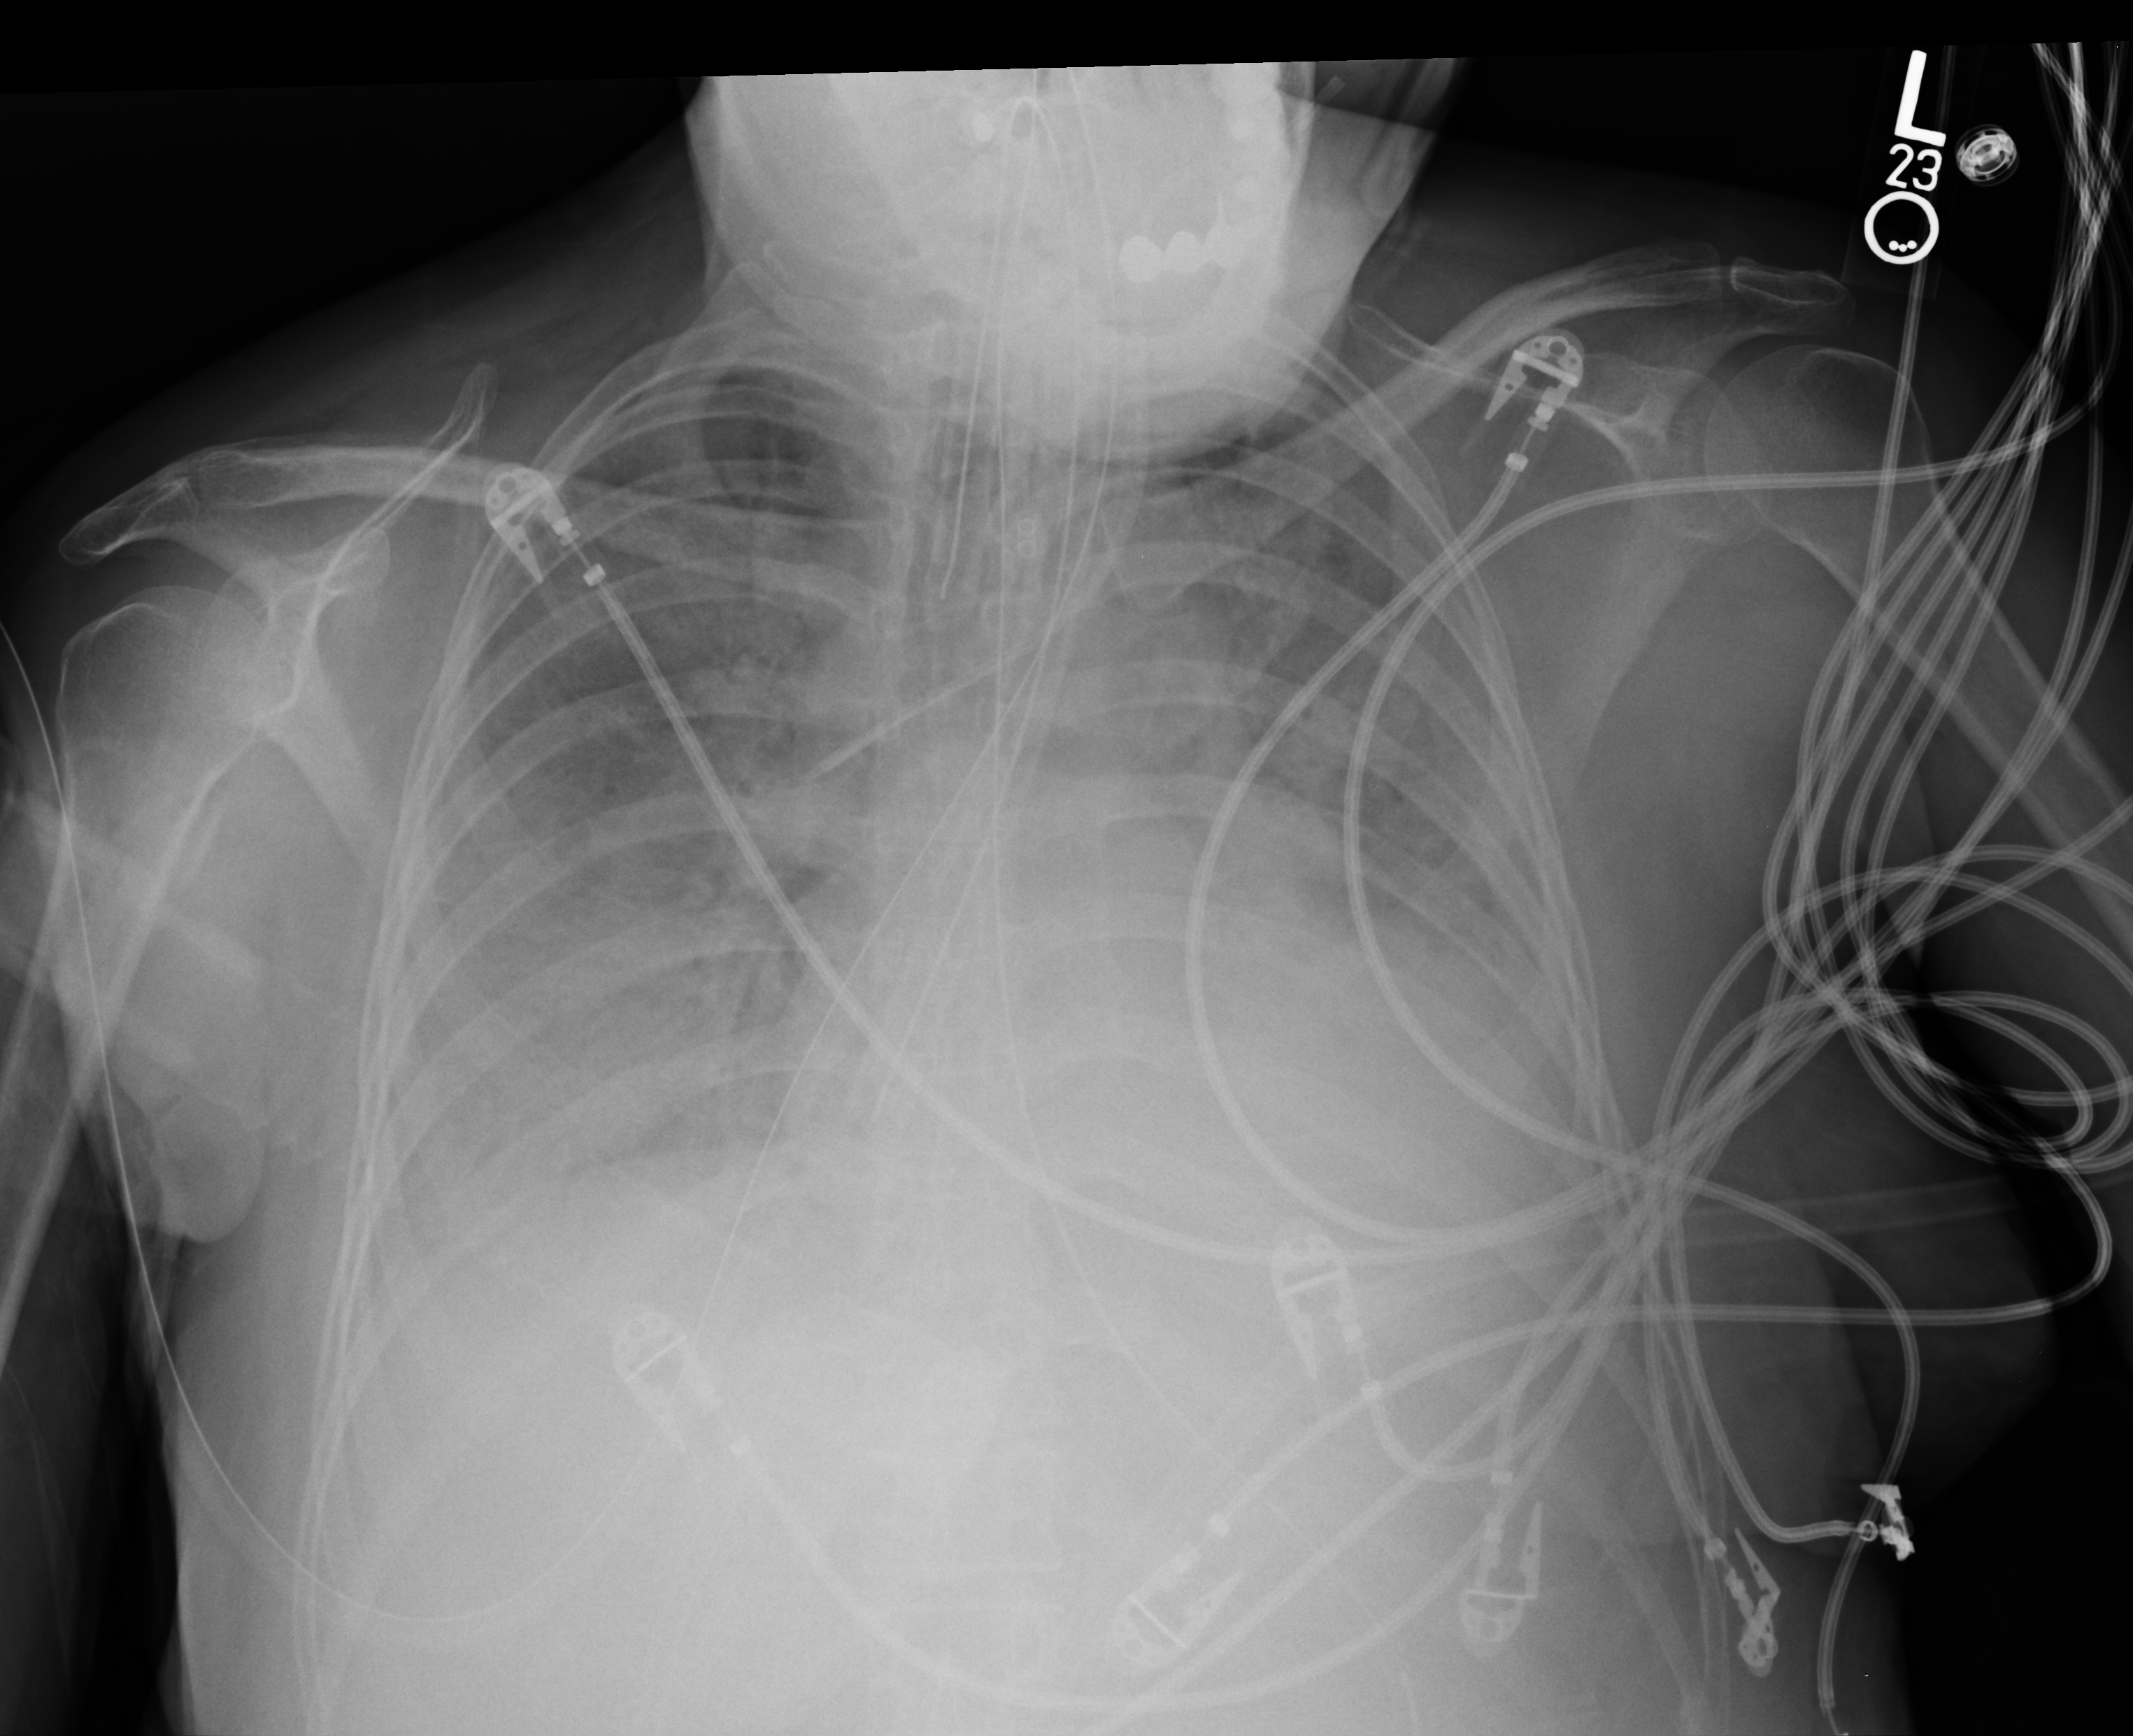
Bedside chest radiograph (computed radiography); anteroposterior (AP) projection. Patient hospitalised with COVID-19, aged 18–59 years.
Hospital-stay facts (about this admission, not read from this image; timing relative to this image not recorded):
- admitted to intensive care during this hospital stay: yes